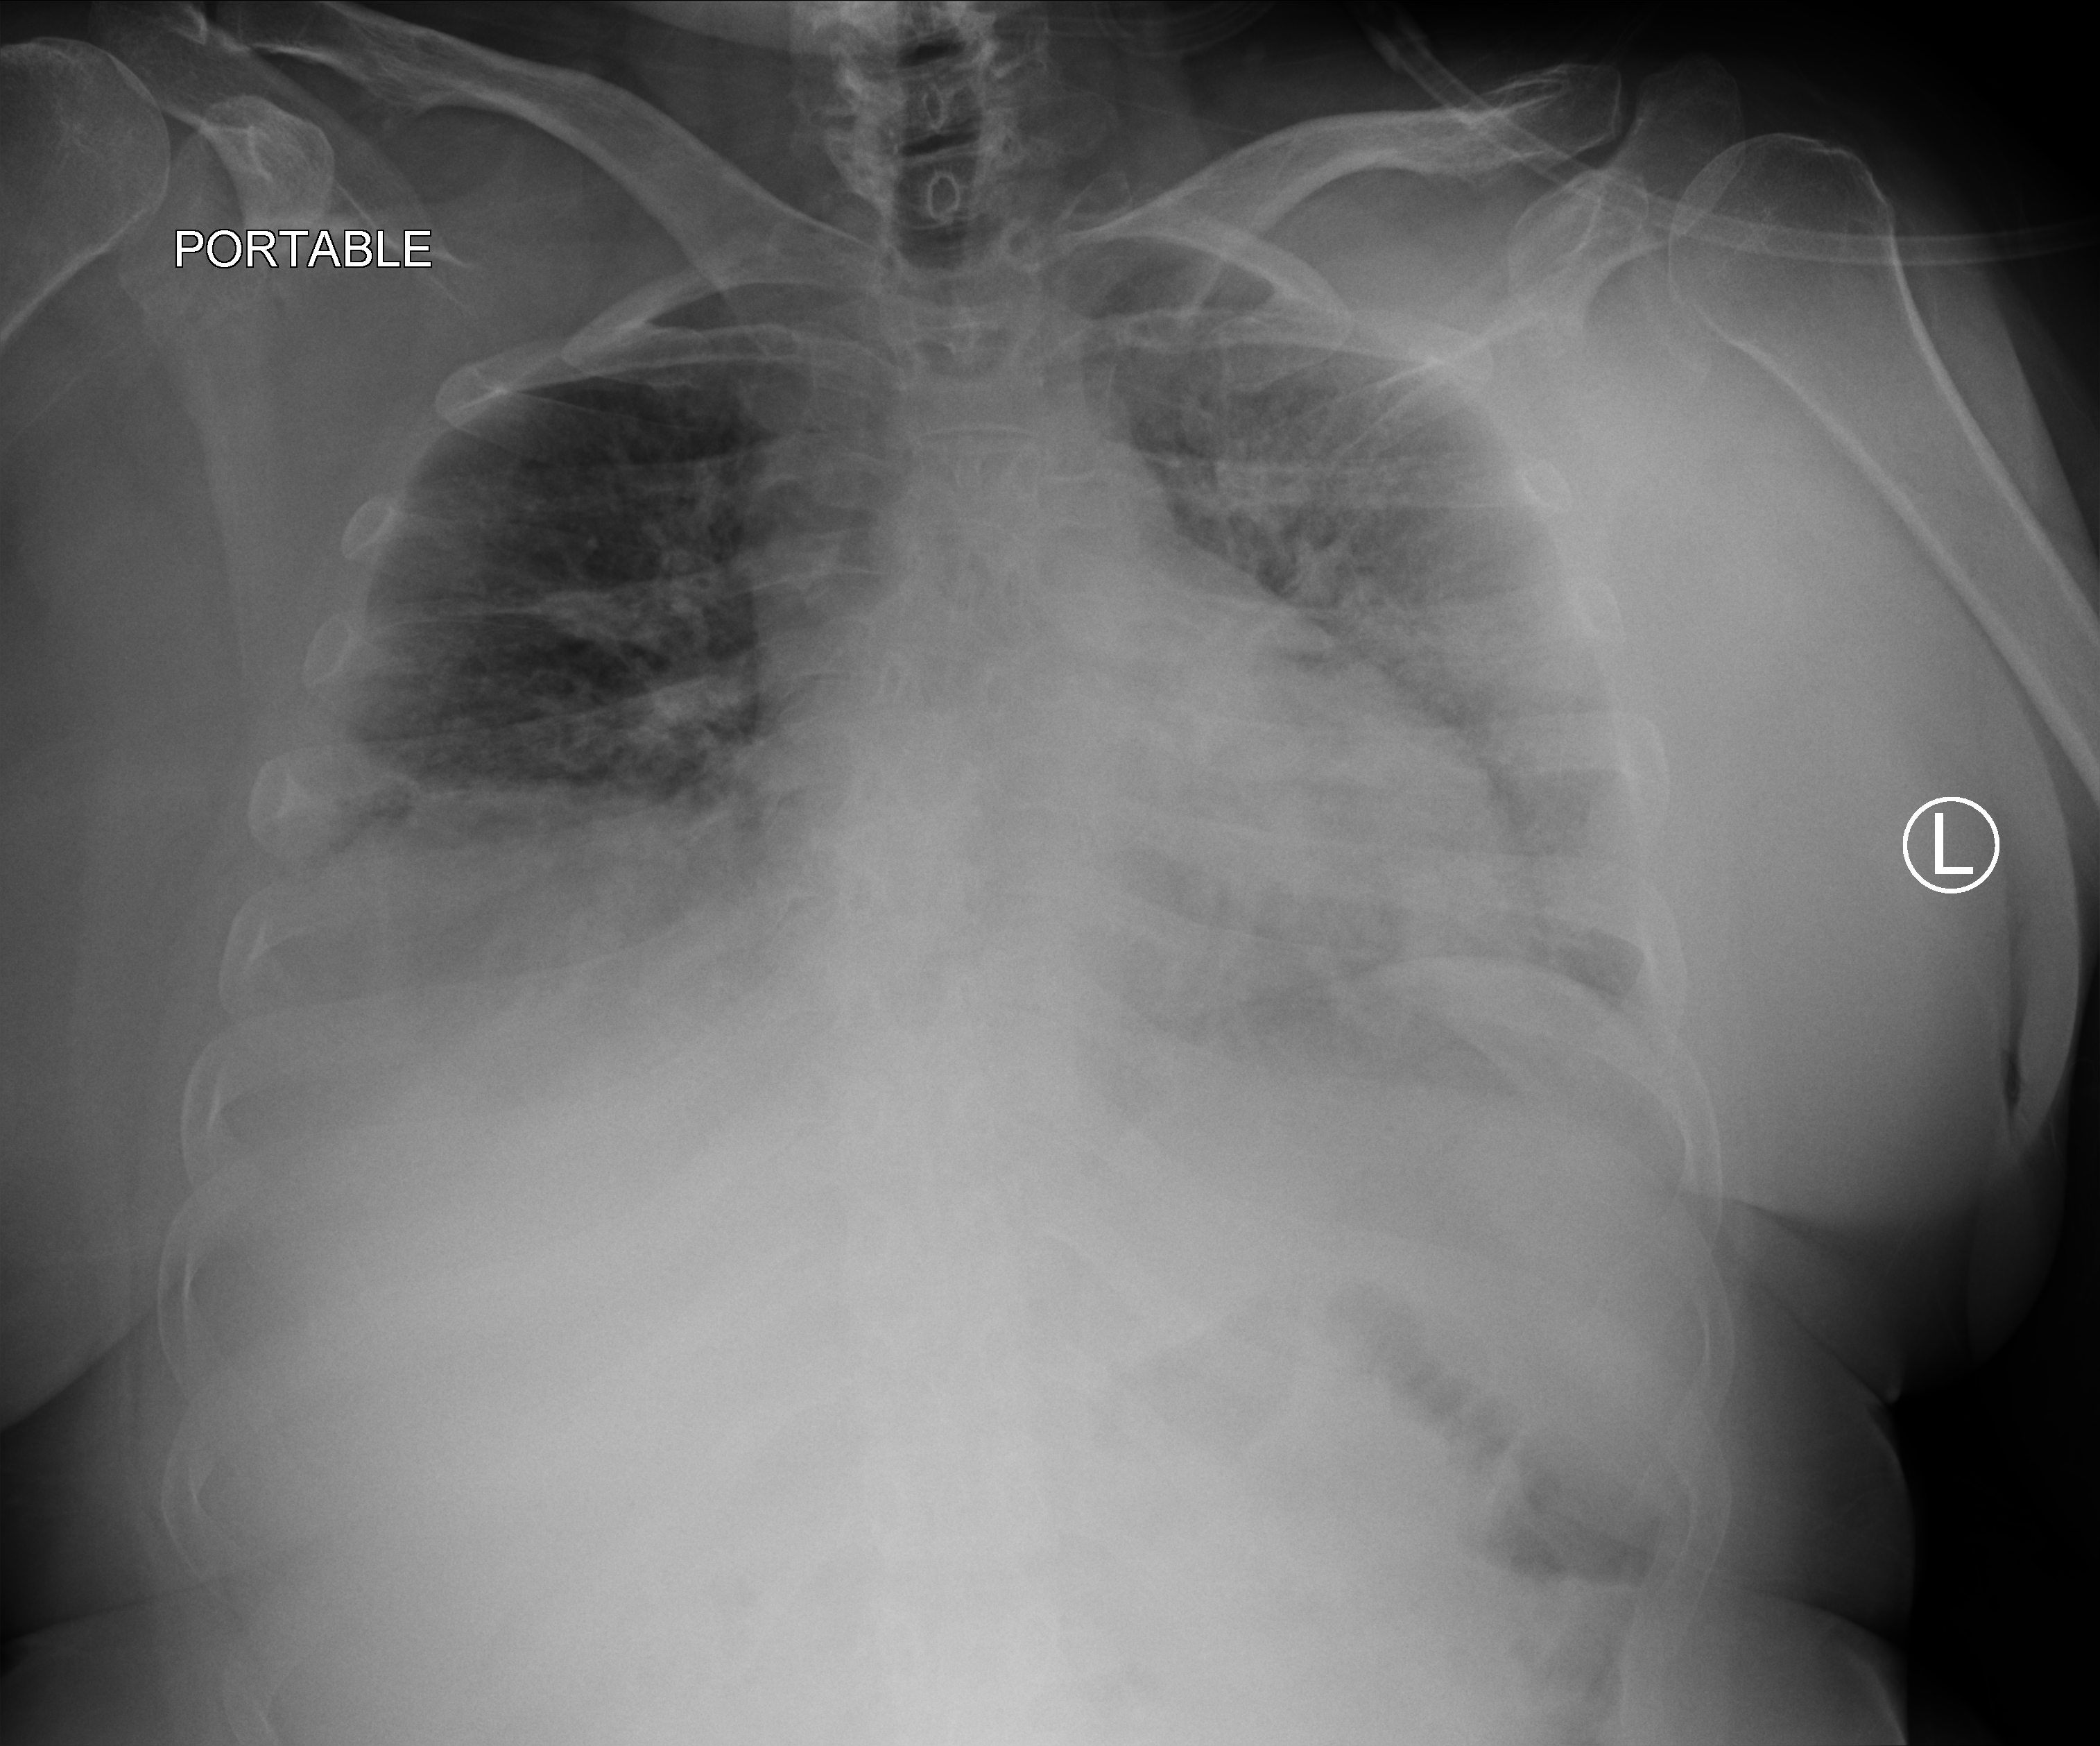
Bedside chest radiograph (computed radiography). Patient hospitalised with COVID-19; female, aged 18–59 years.
Admission-level facts for this patient (not findings on this image; timing relative to this image not recorded):
- mechanically ventilated during this hospital stay: no
- length of hospital stay: 15 days